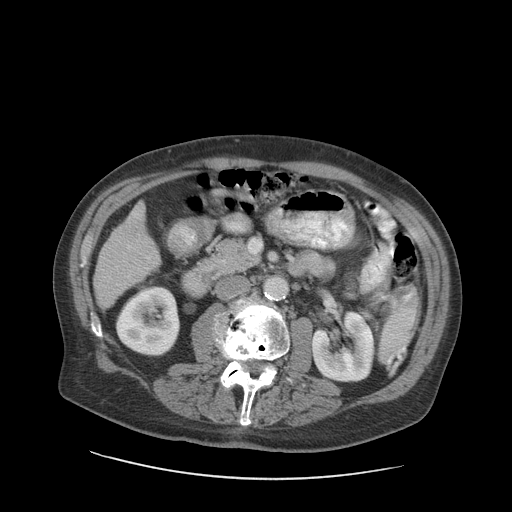
Contrast-enhanced abdominal CT (liver protocol), one axial slice; position 32 of 89 along the scan axis; reconstruction kernel STANDARD; 140 kVp; soft-tissue window (W 400 / L 40 HU); 2.5 mm slice thickness; 512 × 512 image matrix, field of view 420 × 420 mm. From the clinical record (not read from this slice): diagnosis: hepatocellular carcinoma (patient treated with transarterial chemoembolisation; whether this scan precedes or follows treatment is not stated here); TNM stage (as recorded): Stage-I; Child-Pugh class: A.
Annotated regions visible in this slice (semi-automatically segmented with operator editing):
- liver parenchyma outside the tumour (the mass and vessels are separate outlines, so this box may not span the whole liver): bounding box <94,202,160,309> (left, top, right, bottom; pixels)
- mass: <123,216,144,236>
- liver vessels: <127,213,150,259>